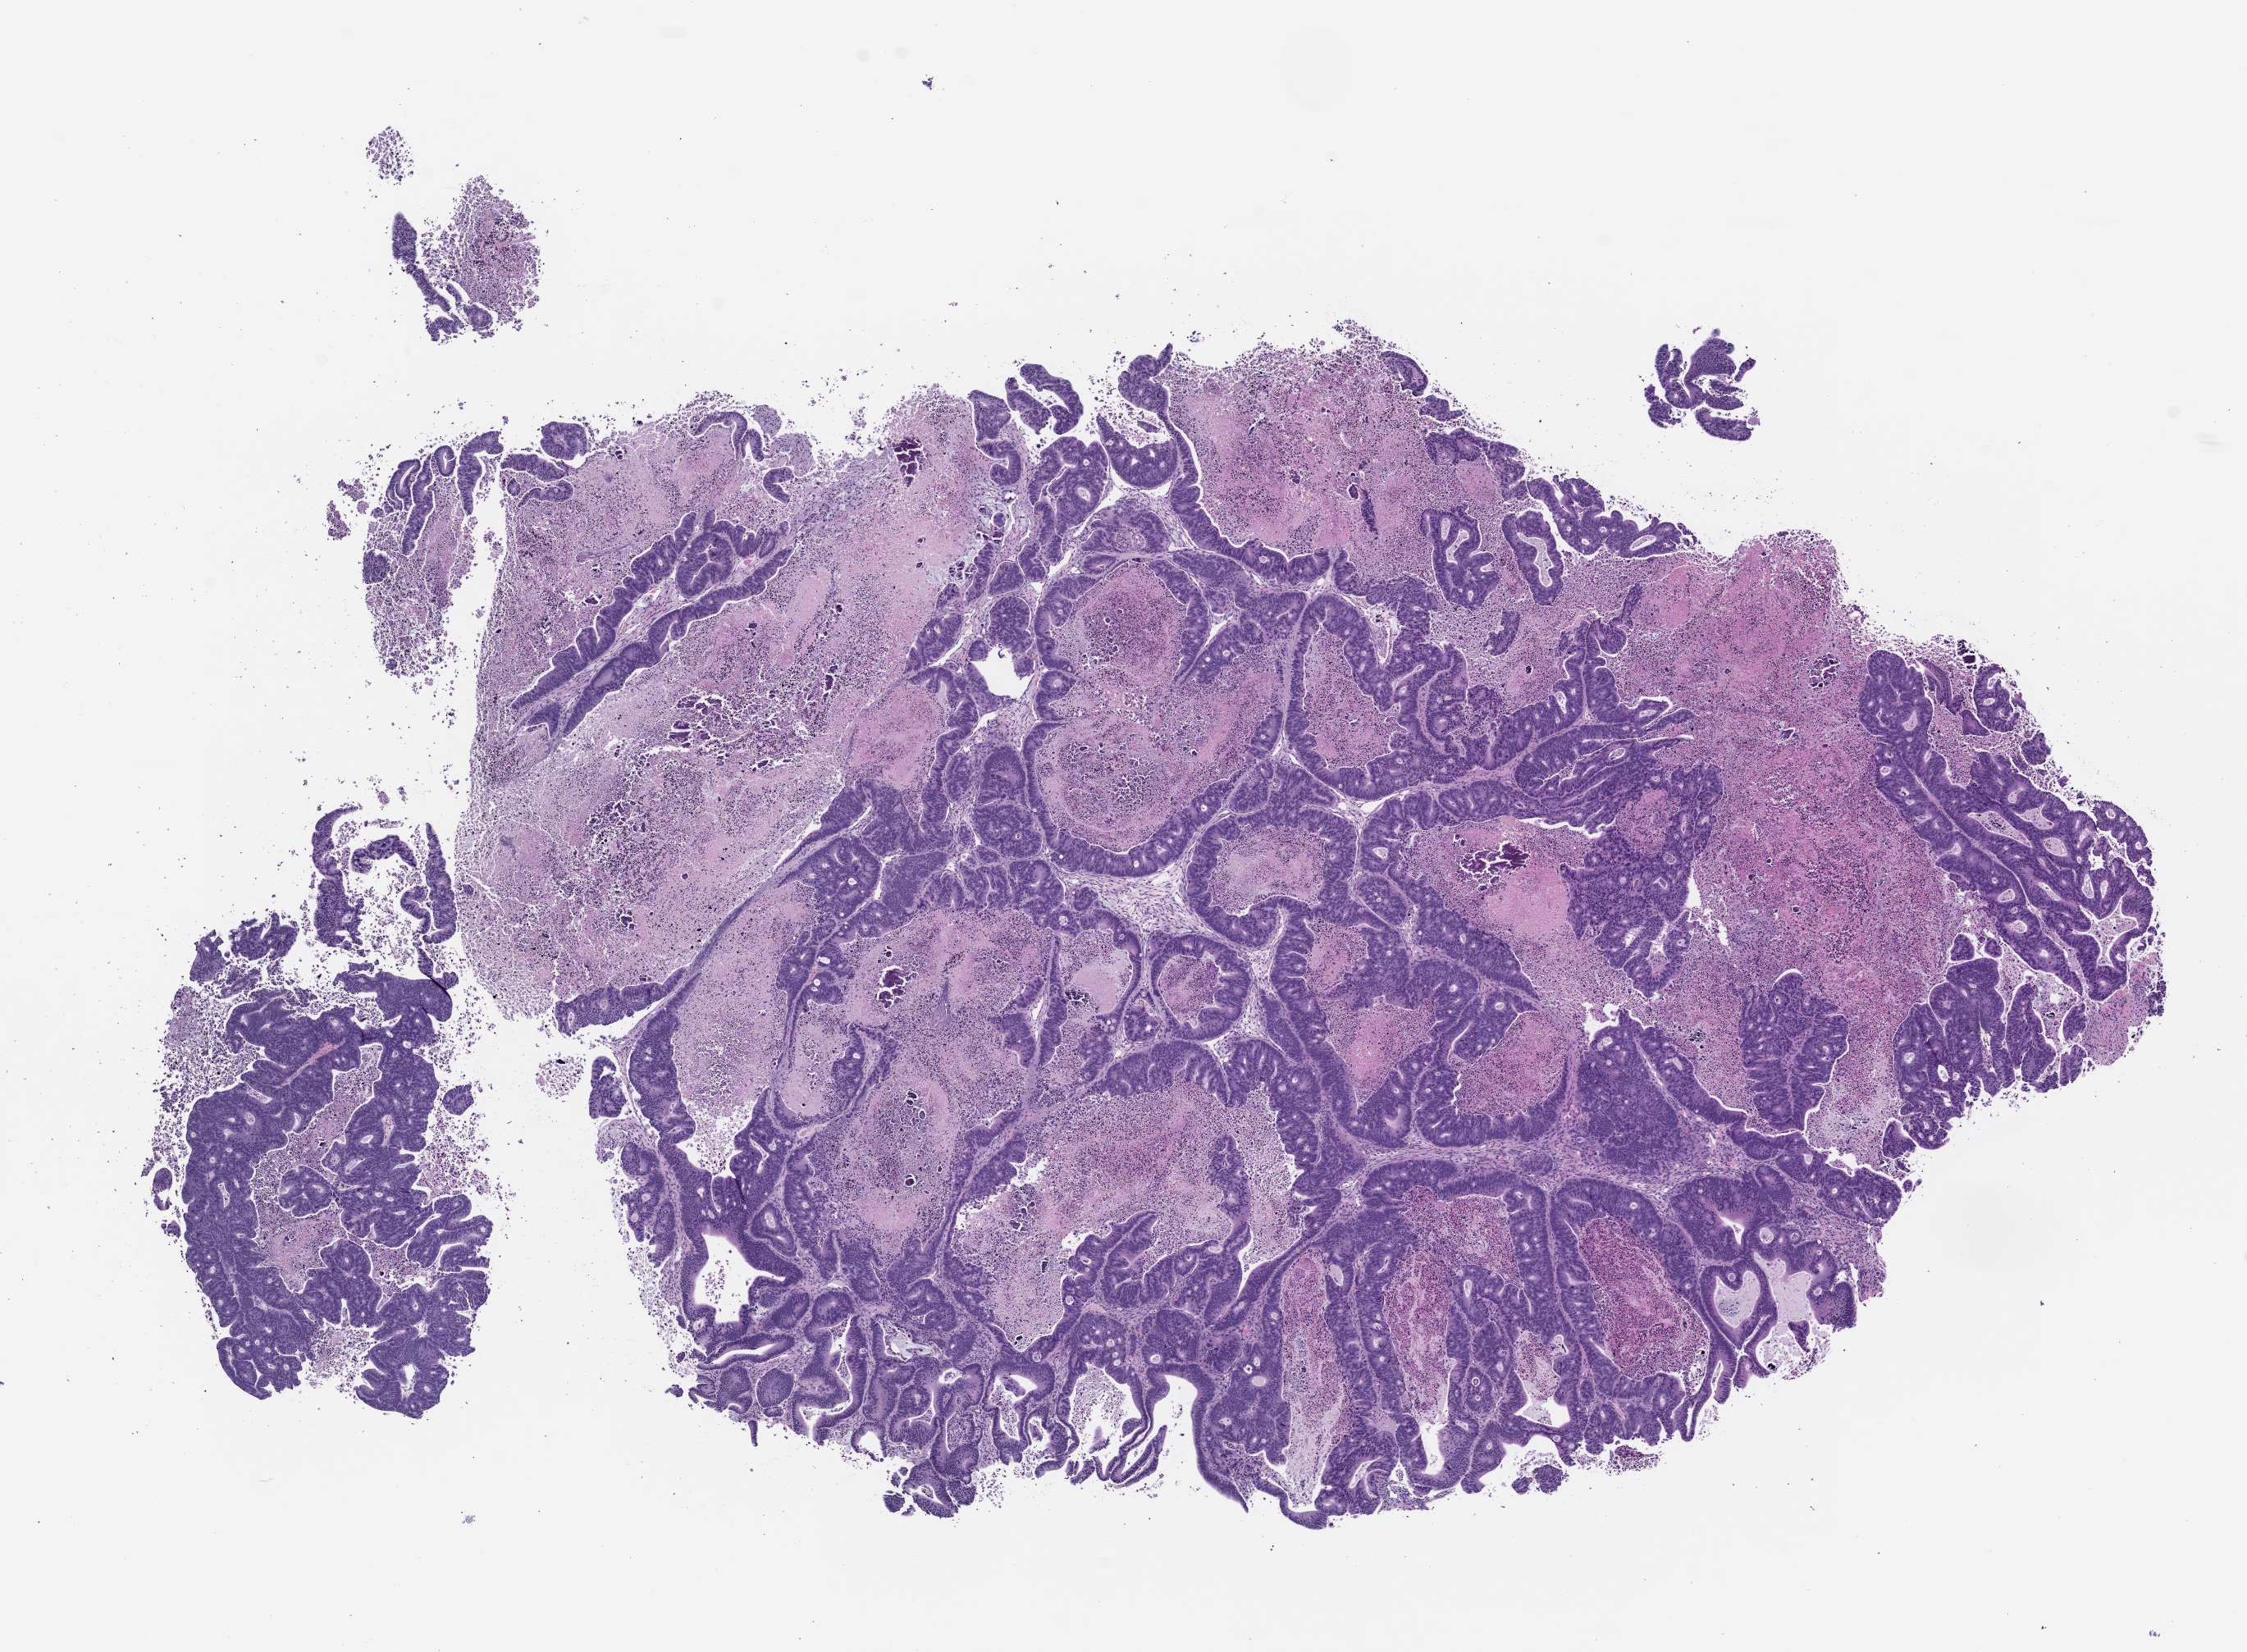
Hematoxylin and eosin (H&E) whole-slide image of a patient-derived xenograft (PDX) tumor grown in a mouse, passage 1 — shown as a low-resolution overview of the whole scanned area (about 11.0 x 8.1 mm), formalin-fixed paraffin-embedded section, originating tumor site category: colon.
Originating patient diagnosis: Colon Adenocarcinoma.